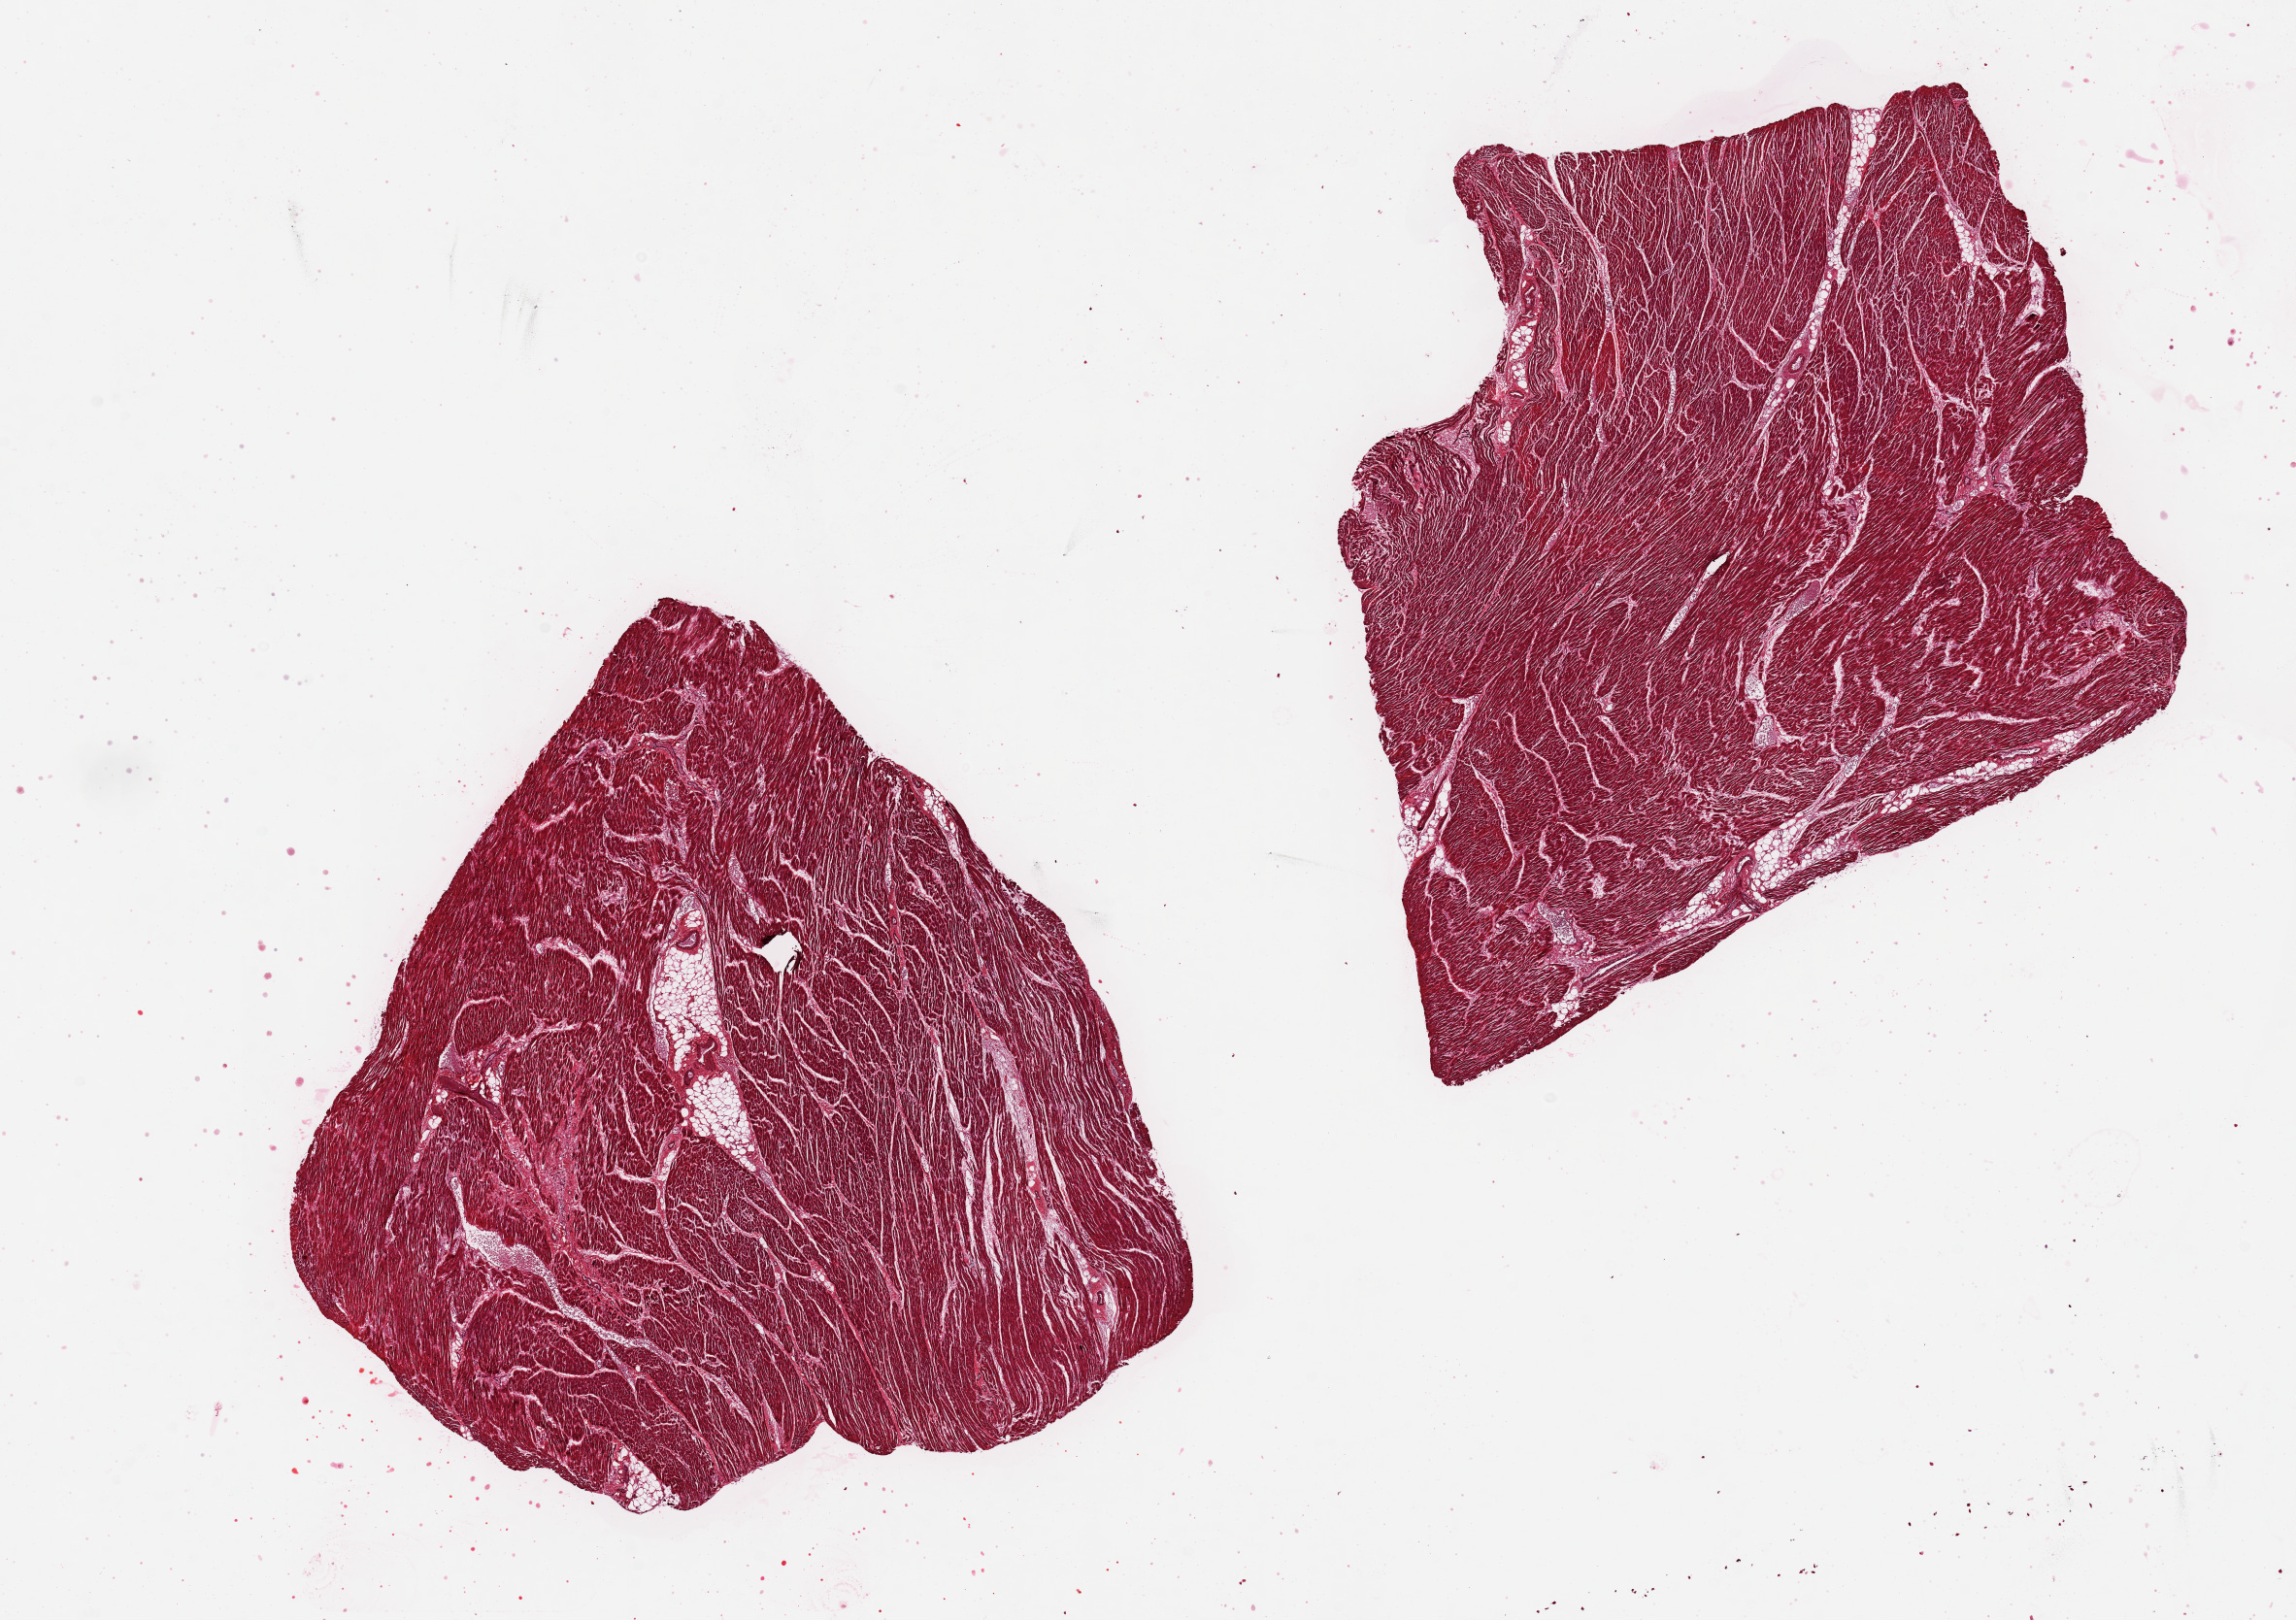
Digitized haematoxylin and eosin-stained section, brightfield — low-resolution overview of the scanned area, about 18.7 x 13.2 mm (acquisition: 20x scan), PAXgene-fixed paraffin-embedded (PFPE) section, section of heart (target tissue), tissue donor sample. Donor sex: male.
Review note (as recorded): 2 pieces 7x6 & 7x5 mm; <10% internal adipose.